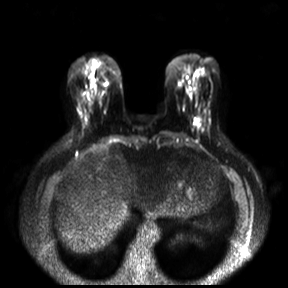
Breast MRI, one axial slice; position 8 of 30 along the scan axis; diffusion-weighted series; image 2 of 4 stored at this slice position (different b-values; order by instance number); 3 T; 288 × 288 image matrix, field of view 360 × 360 mm. Female patient.
Annotated regions visible in this slice (expert manual segmentation):
- tumour on diffusion-weighted imaging: bounding box [x1, y1, x2, y2] px = [195, 120, 199, 124]